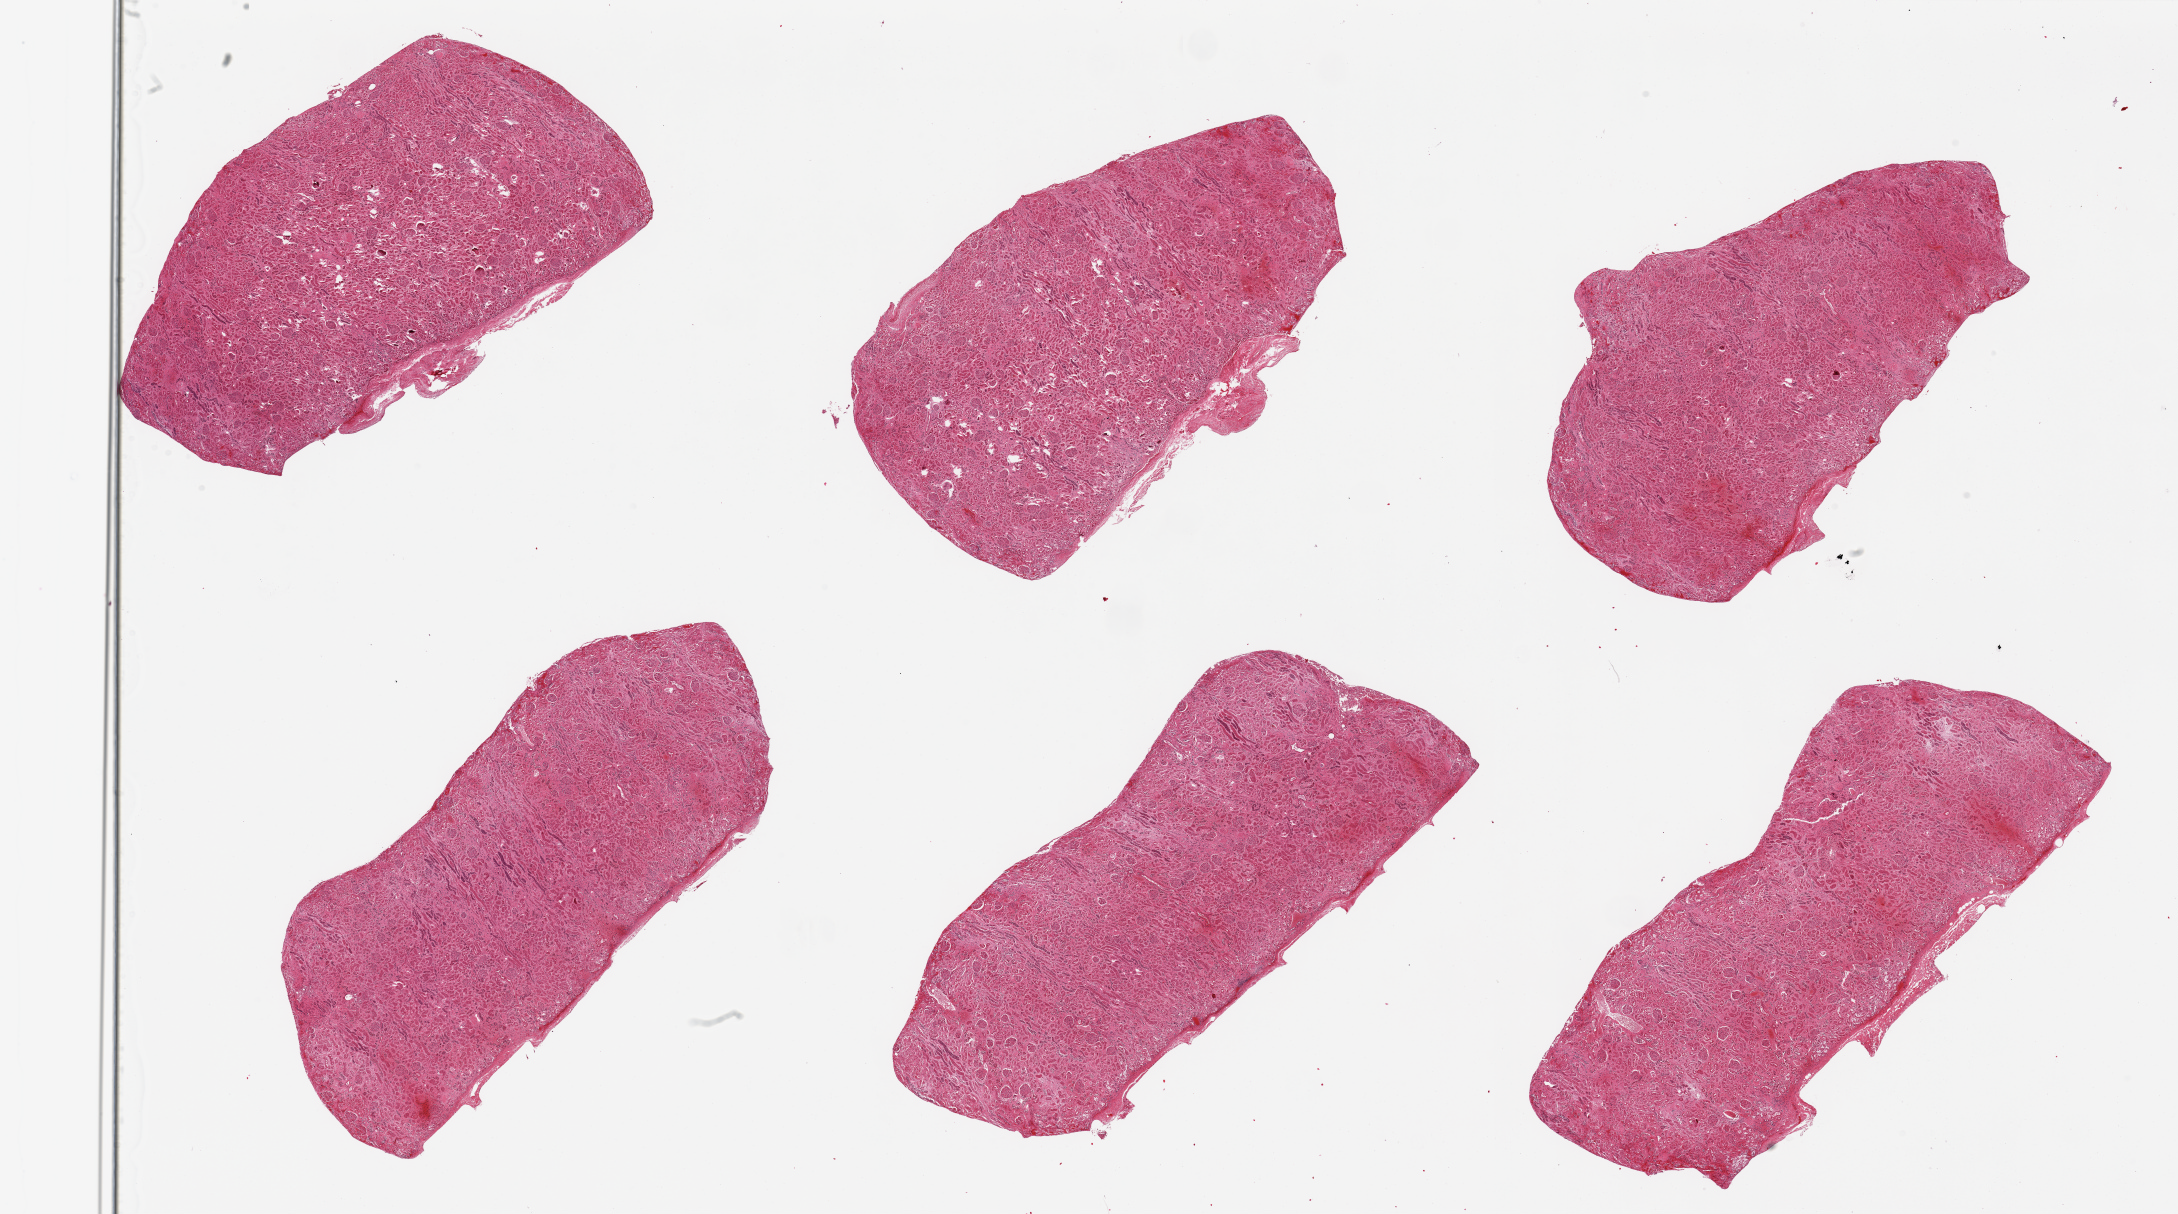
Digitized hematoxylin and eosin (H&E)-stained section, brightfield — whole scanned area (about 34.5 x 19.2 mm, from a 20x scan) shown as a low-resolution overview, PAXgene-fixed paraffin-embedded (PFPE) section, sampled site (target tissue): renal cortex, donor tissue sample. Donor: female.
• pathologist's review note for this sample: 6 pieces; tubules very autolyzed